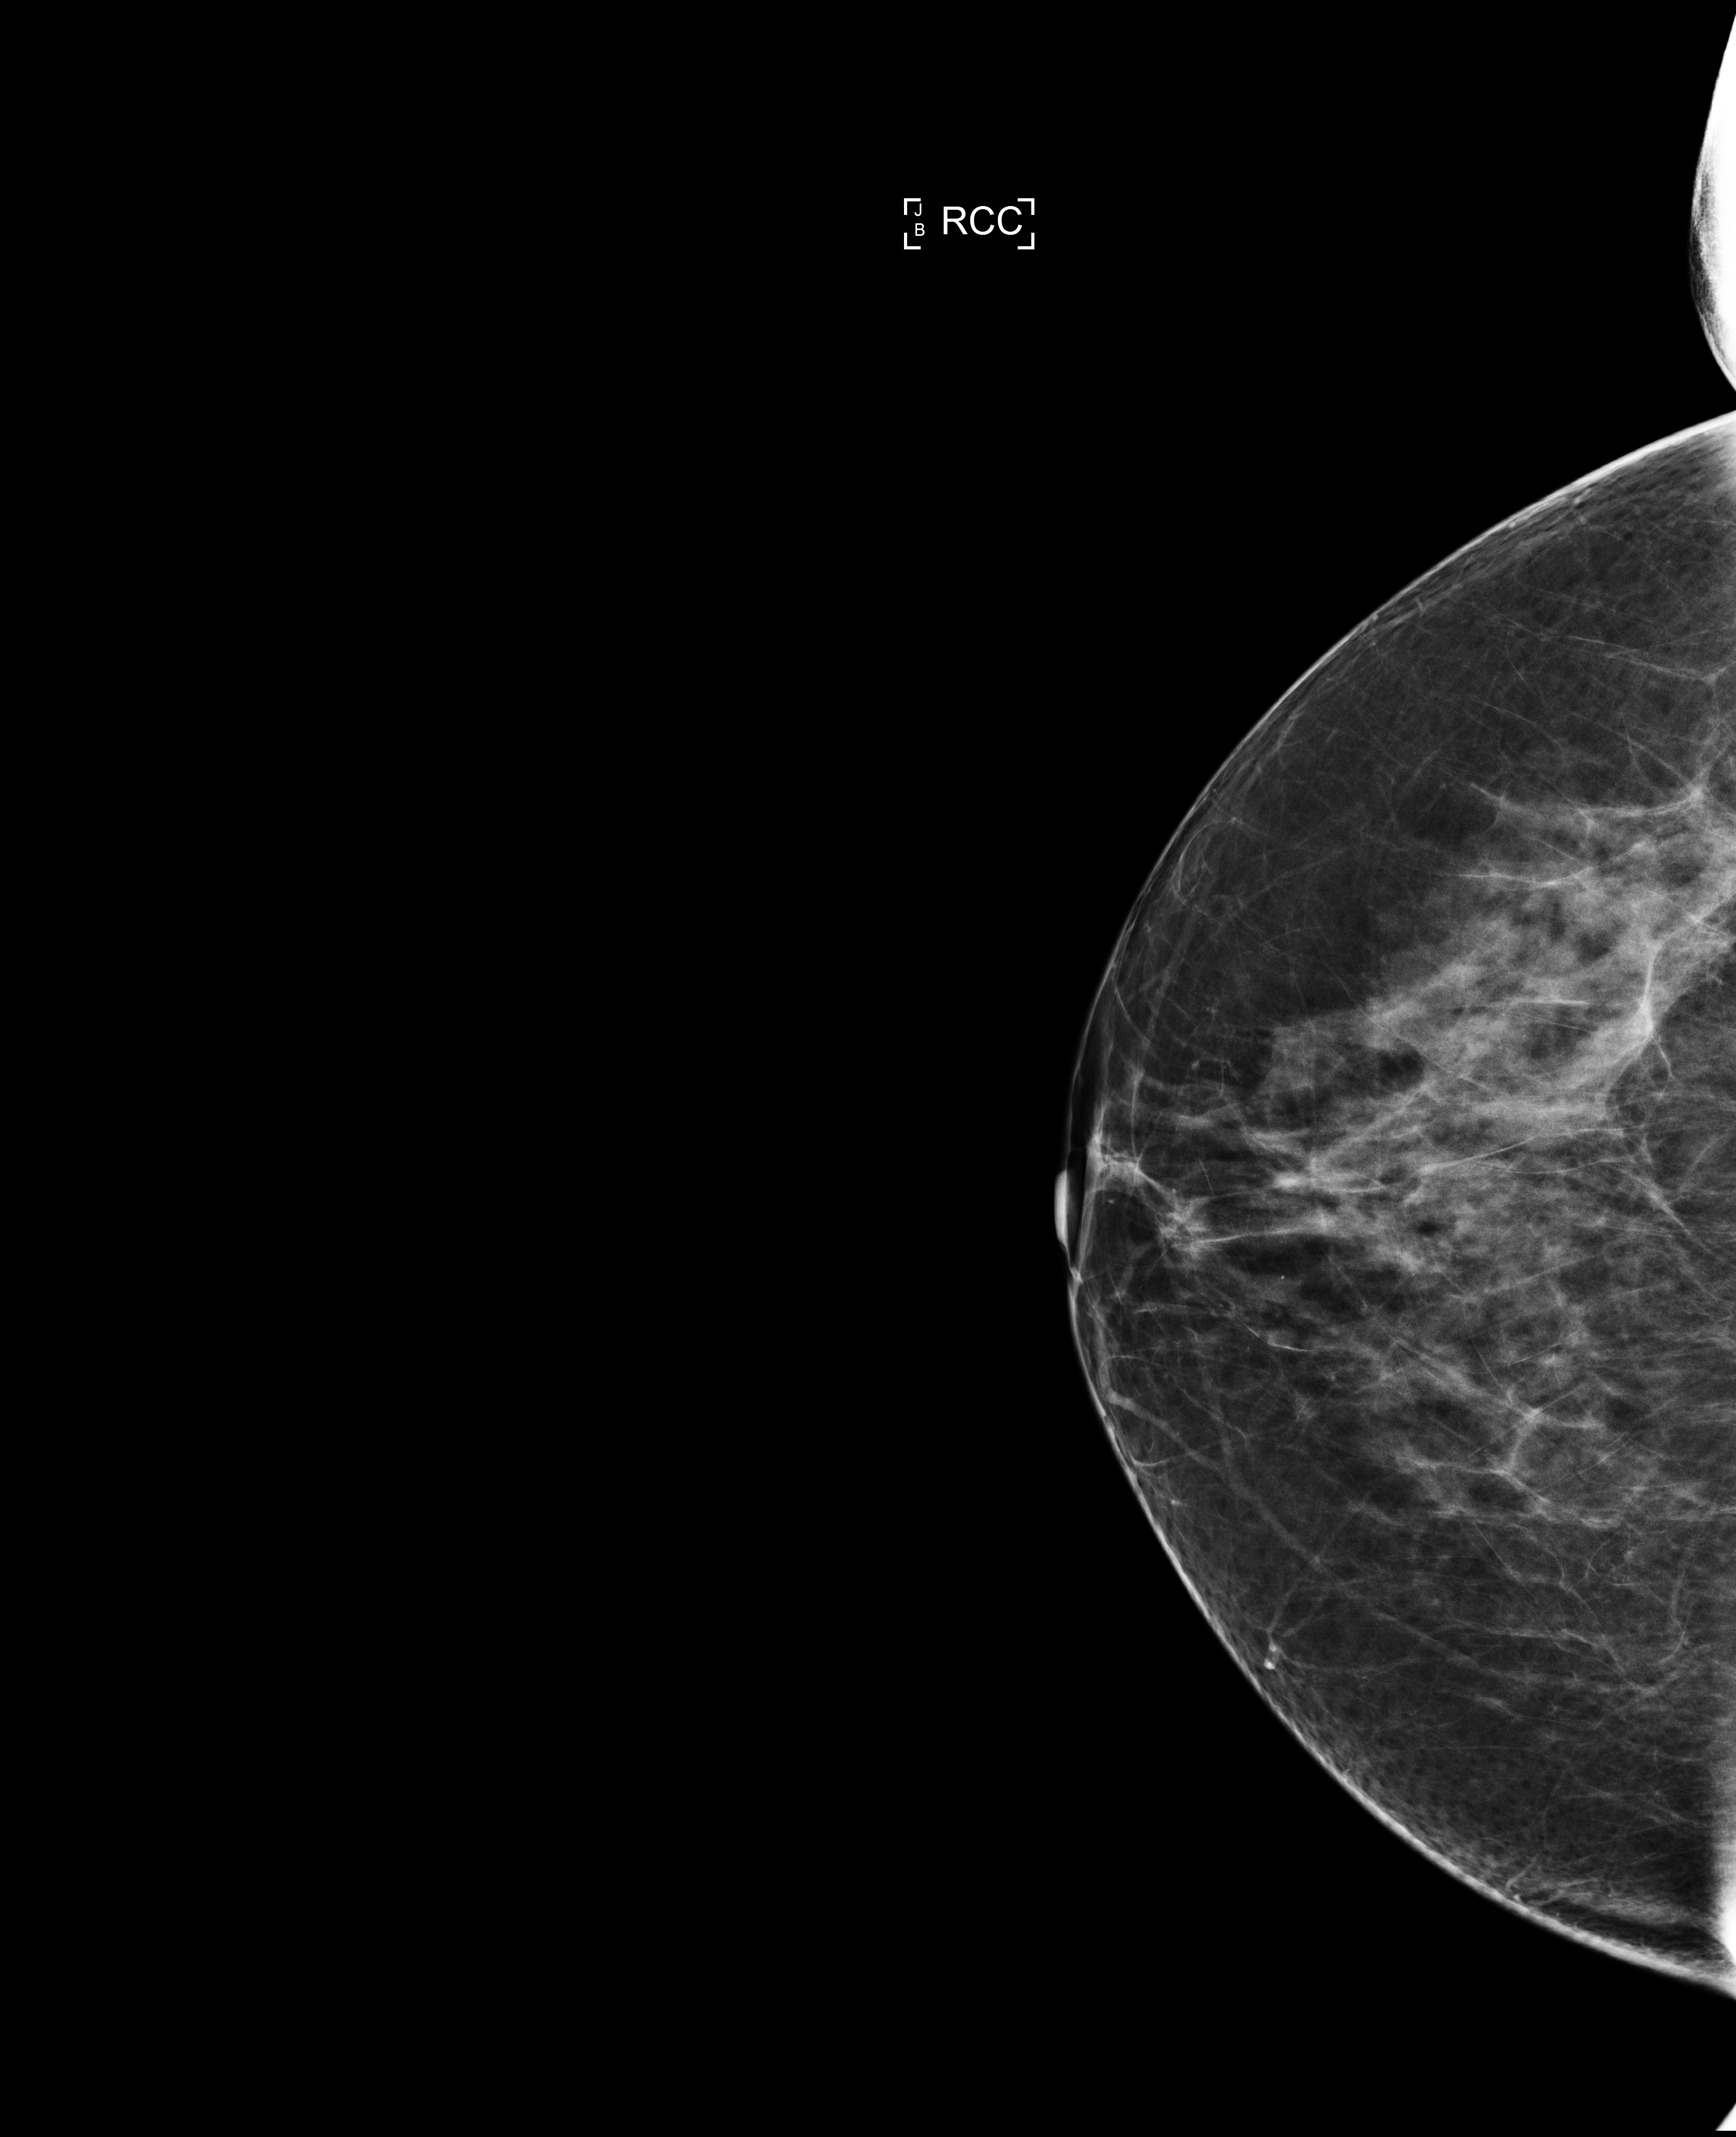
Digital mammogram (FFDM); right breast; CC view; screening examination; compressed breast thickness 67 mm. Patient: female, 55 years.
- breast density at the screening exam (both breasts): heterogeneously dense (BI-RADS density category c)
- final BI-RADS category for the screening round (tomosynthesis exam, both breasts): category 1
- recall: no recall after this screen